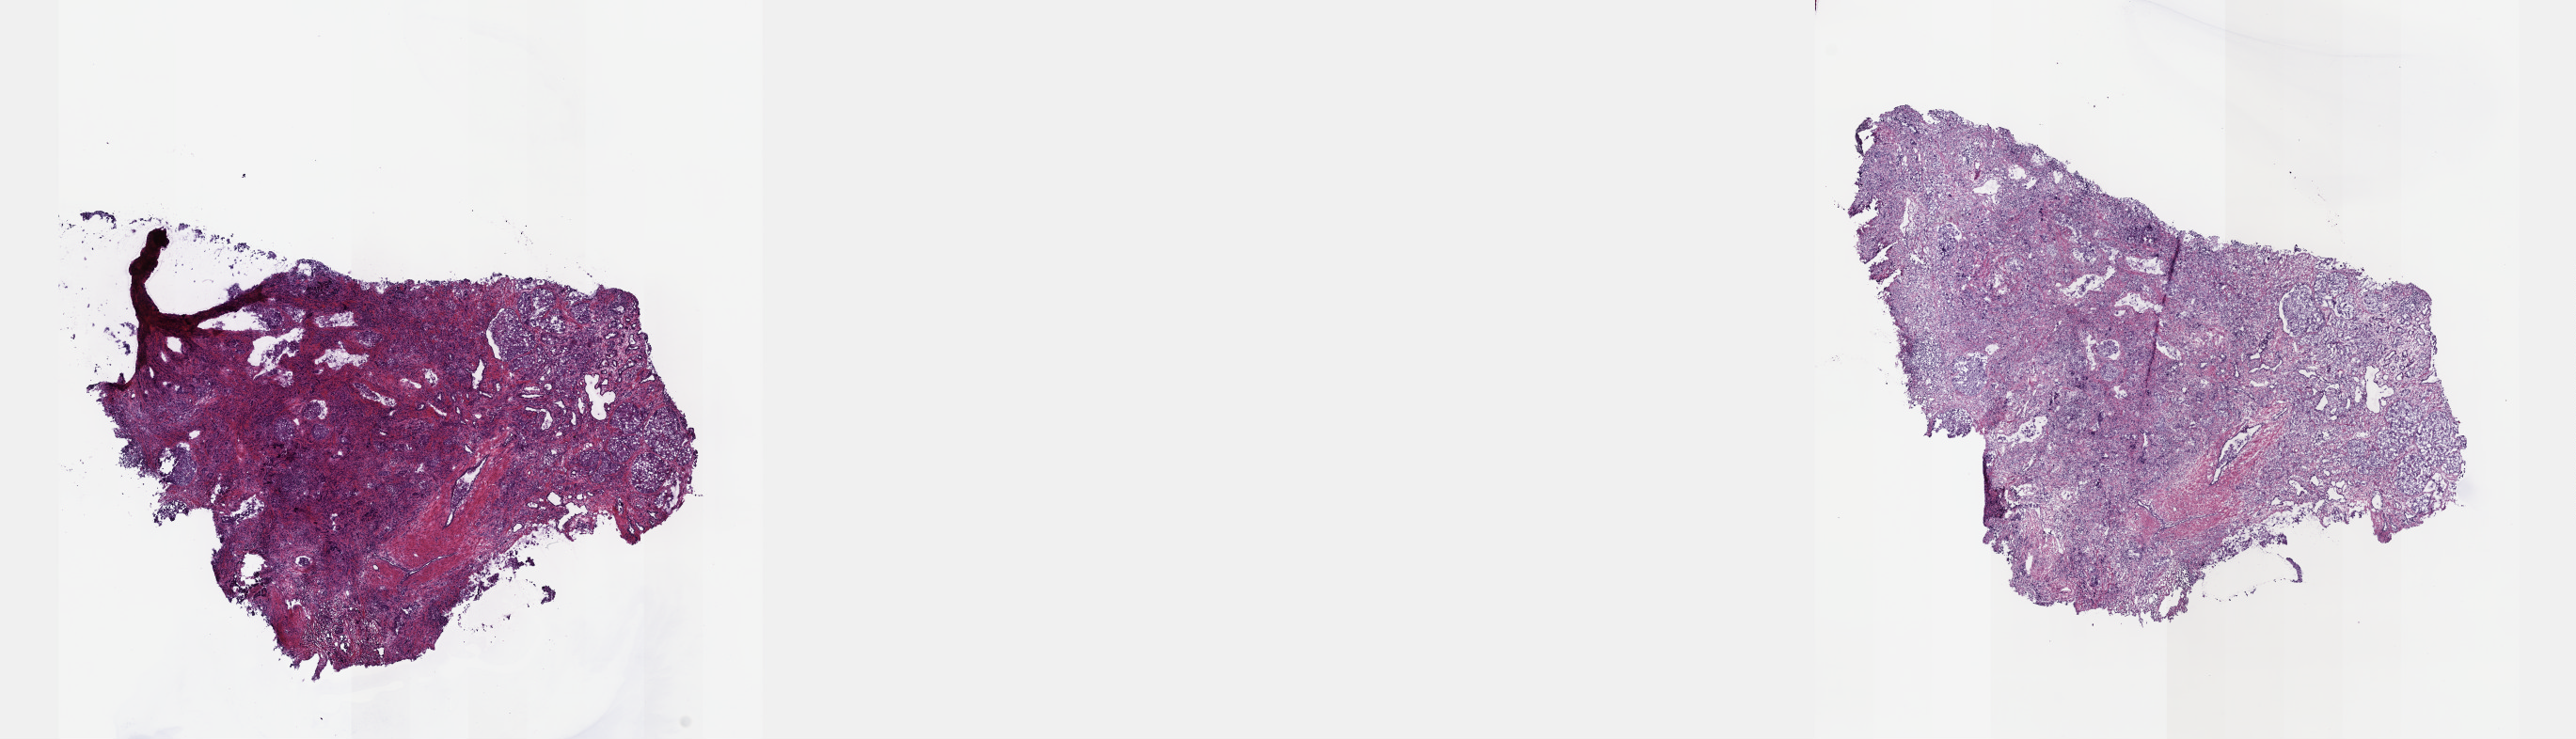
Whole-slide histology image, H&E-stained, a low-resolution overview of the entire scanned area, about 22.1 x 6.4 mm; frozen section; prostate, primary tumour sample. Male, age 64 years at initial diagnosis. Gleason score: 9 (5+4). Composition of this section per pathologist review: tumour cells 80%, tumour nuclei 90%, normal cells 0%, stromal cells 20%, necrosis 0%. Infiltration values recorded for this section: lymphocyte infiltration 0%, monocyte infiltration 0%, neutrophil infiltration 0%.
Pathologic diagnosis: Adenocarcinoma, NOS (prostate gland). Laterality: bilateral. Lymph nodes positive (case pathology): 6 of 20 examined.